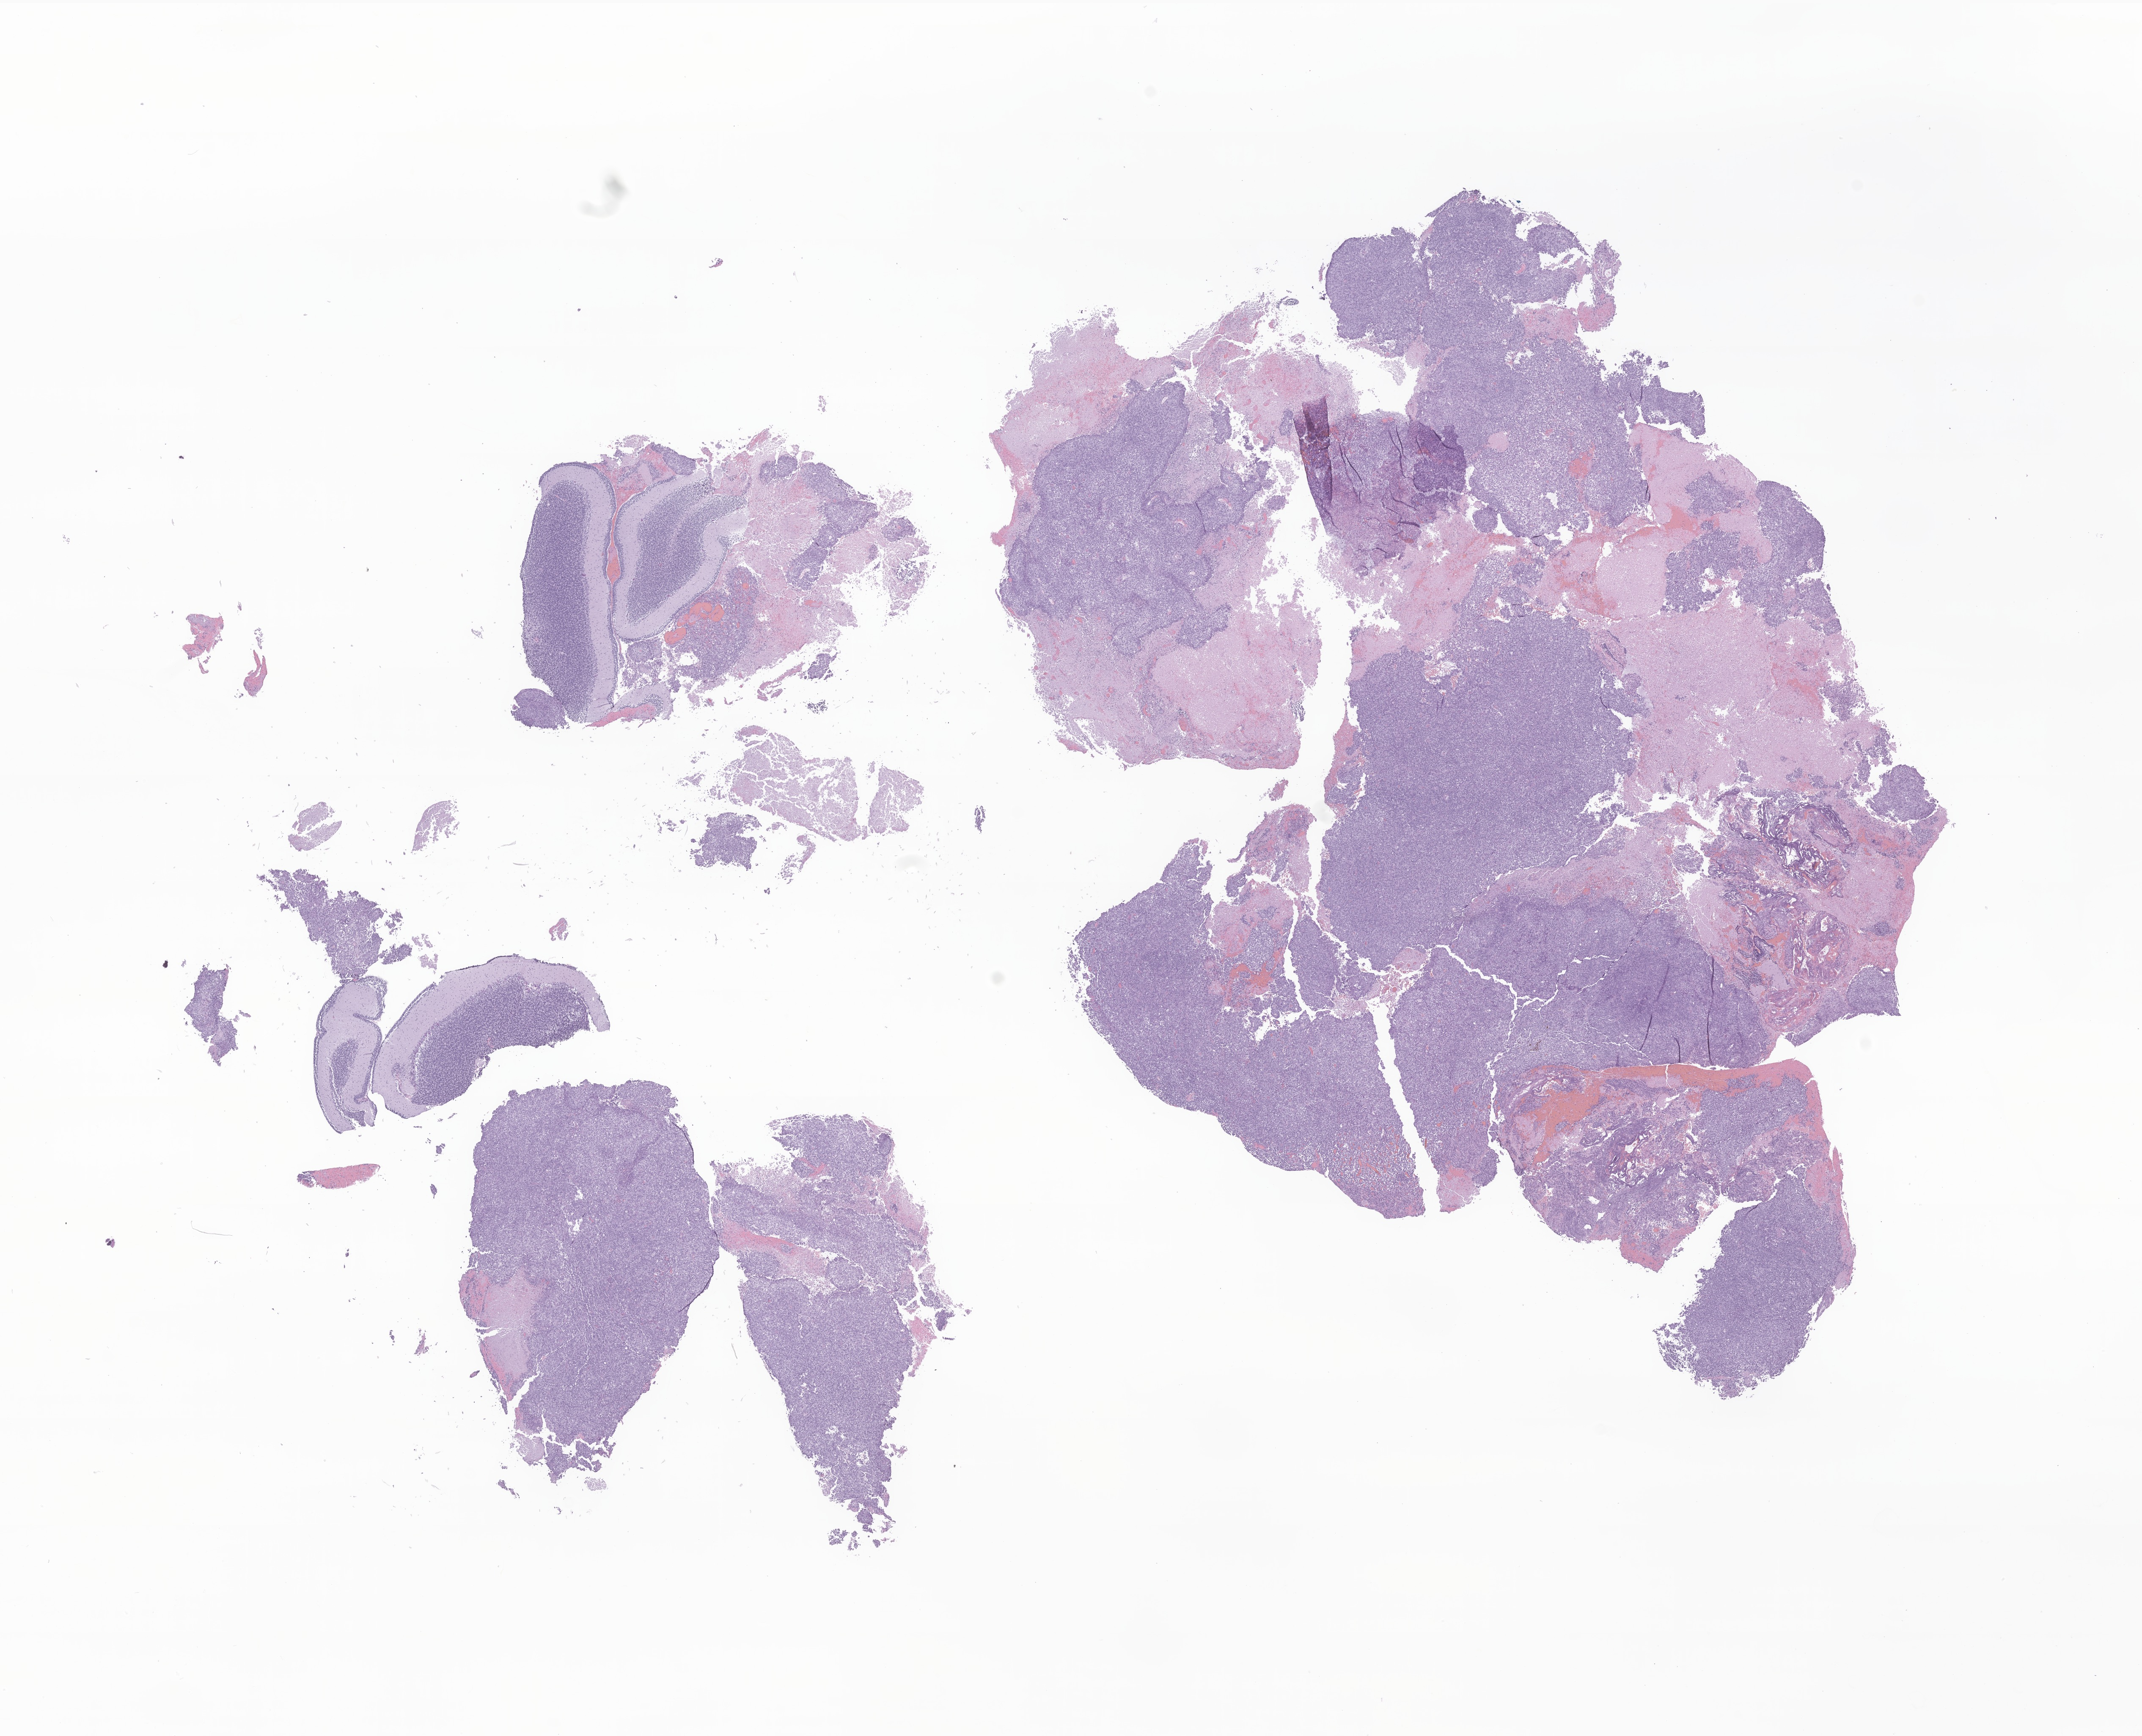
Whole-slide image, H&E stain of tumor tissue from the cerebellum — low-resolution overview of the scanned area, about 21.3 x 17.3 mm. Formalin-fixed, paraffin-embedded (FFPE) tissue. Male patient, age 135 days.
Diagnosis (ICD-O-3 morphology term): Atypical teratoid/rhabdoid tumor.